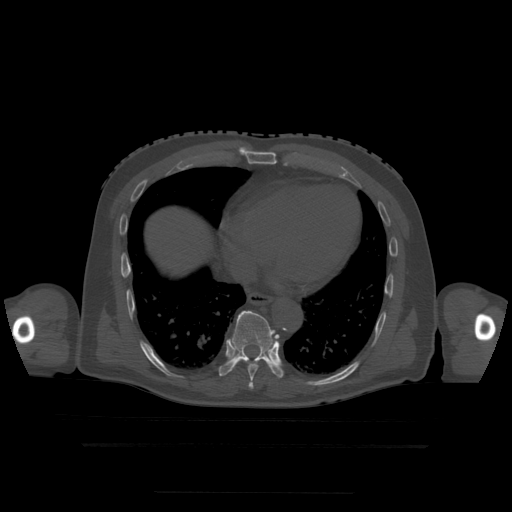
CT including the spine, one axial slice; position 269 of 522 along the scan axis; bone window (W 1800 / L 400 HU); 512 × 512 image matrix, field of view 436 × 436 mm. Patient age 68 years. Case-level facts recorded for this patient, not image findings: primary cancer: urothelial.
Annotated regions visible in this slice (semi-automatic segmentation, software-assisted and operator-edited):
- T7 vertebra: bounding box (x1, y1, x2, y2) in pixels: (249, 382, 254, 389)
- T8 vertebra: (247, 359, 272, 382)
- T9 vertebra: (219, 311, 284, 379)